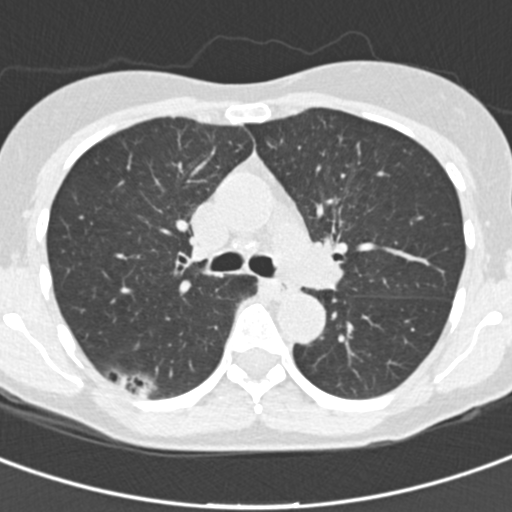
Low-dose screening chest CT, one axial slice; slice 100 of 162 in the series (ordered by position); reconstruction kernel B30f; 120 kVp; lung window (W 1500 / L -600 HU); 2 mm slice thickness; 512 × 512 image matrix.
Outlined on this slice (outlined manually by an expert reader):
- lesion 1 (tumor, lower lobe of right lung): bounding box (x1, y1, x2, y2) in pixels: (137, 384, 150, 398)